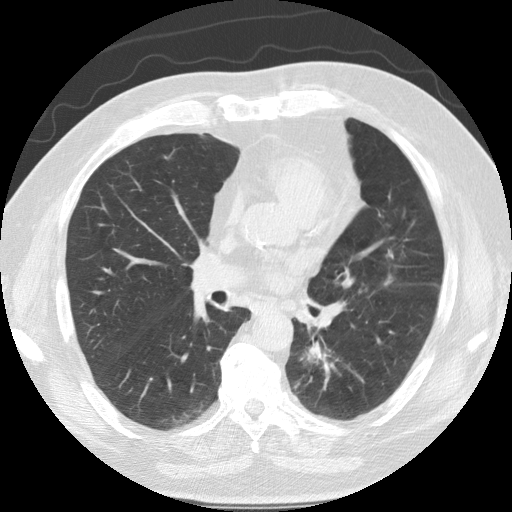
Low-dose screening chest CT, one axial slice; reconstruction kernel STANDARD; 120 kVp; lung window (W 1500 / L -600 HU); 2.5 mm slice thickness; 512 × 512 image matrix, field of view 360 × 360 mm.
Outlined on this slice (expert manual segmentation):
- lesion 1 (tumor, lower lobe of left lung): bounding box [x1, y1, x2, y2] px = [305, 342, 326, 365]